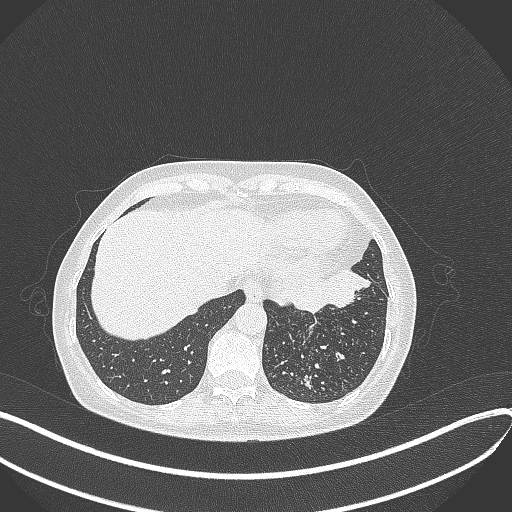
Chest CT, one axial slice; 100 kVp; lung window (W 1500 / L -600 HU); 1 mm slice thickness; 512 × 512 image matrix. Patient: female, 63 years. Case-level facts recorded for this patient, not image findings: clinical TNM (as recorded): T1b N0 M0; histopathological grade: G2-3.
Outlined on this slice (rectangle marked by the reading radiologist):
- lung tumour (recorded histology: adenocarcinoma): bounding box (x1, y1, x2, y2) in pixels: (268, 263, 375, 318)